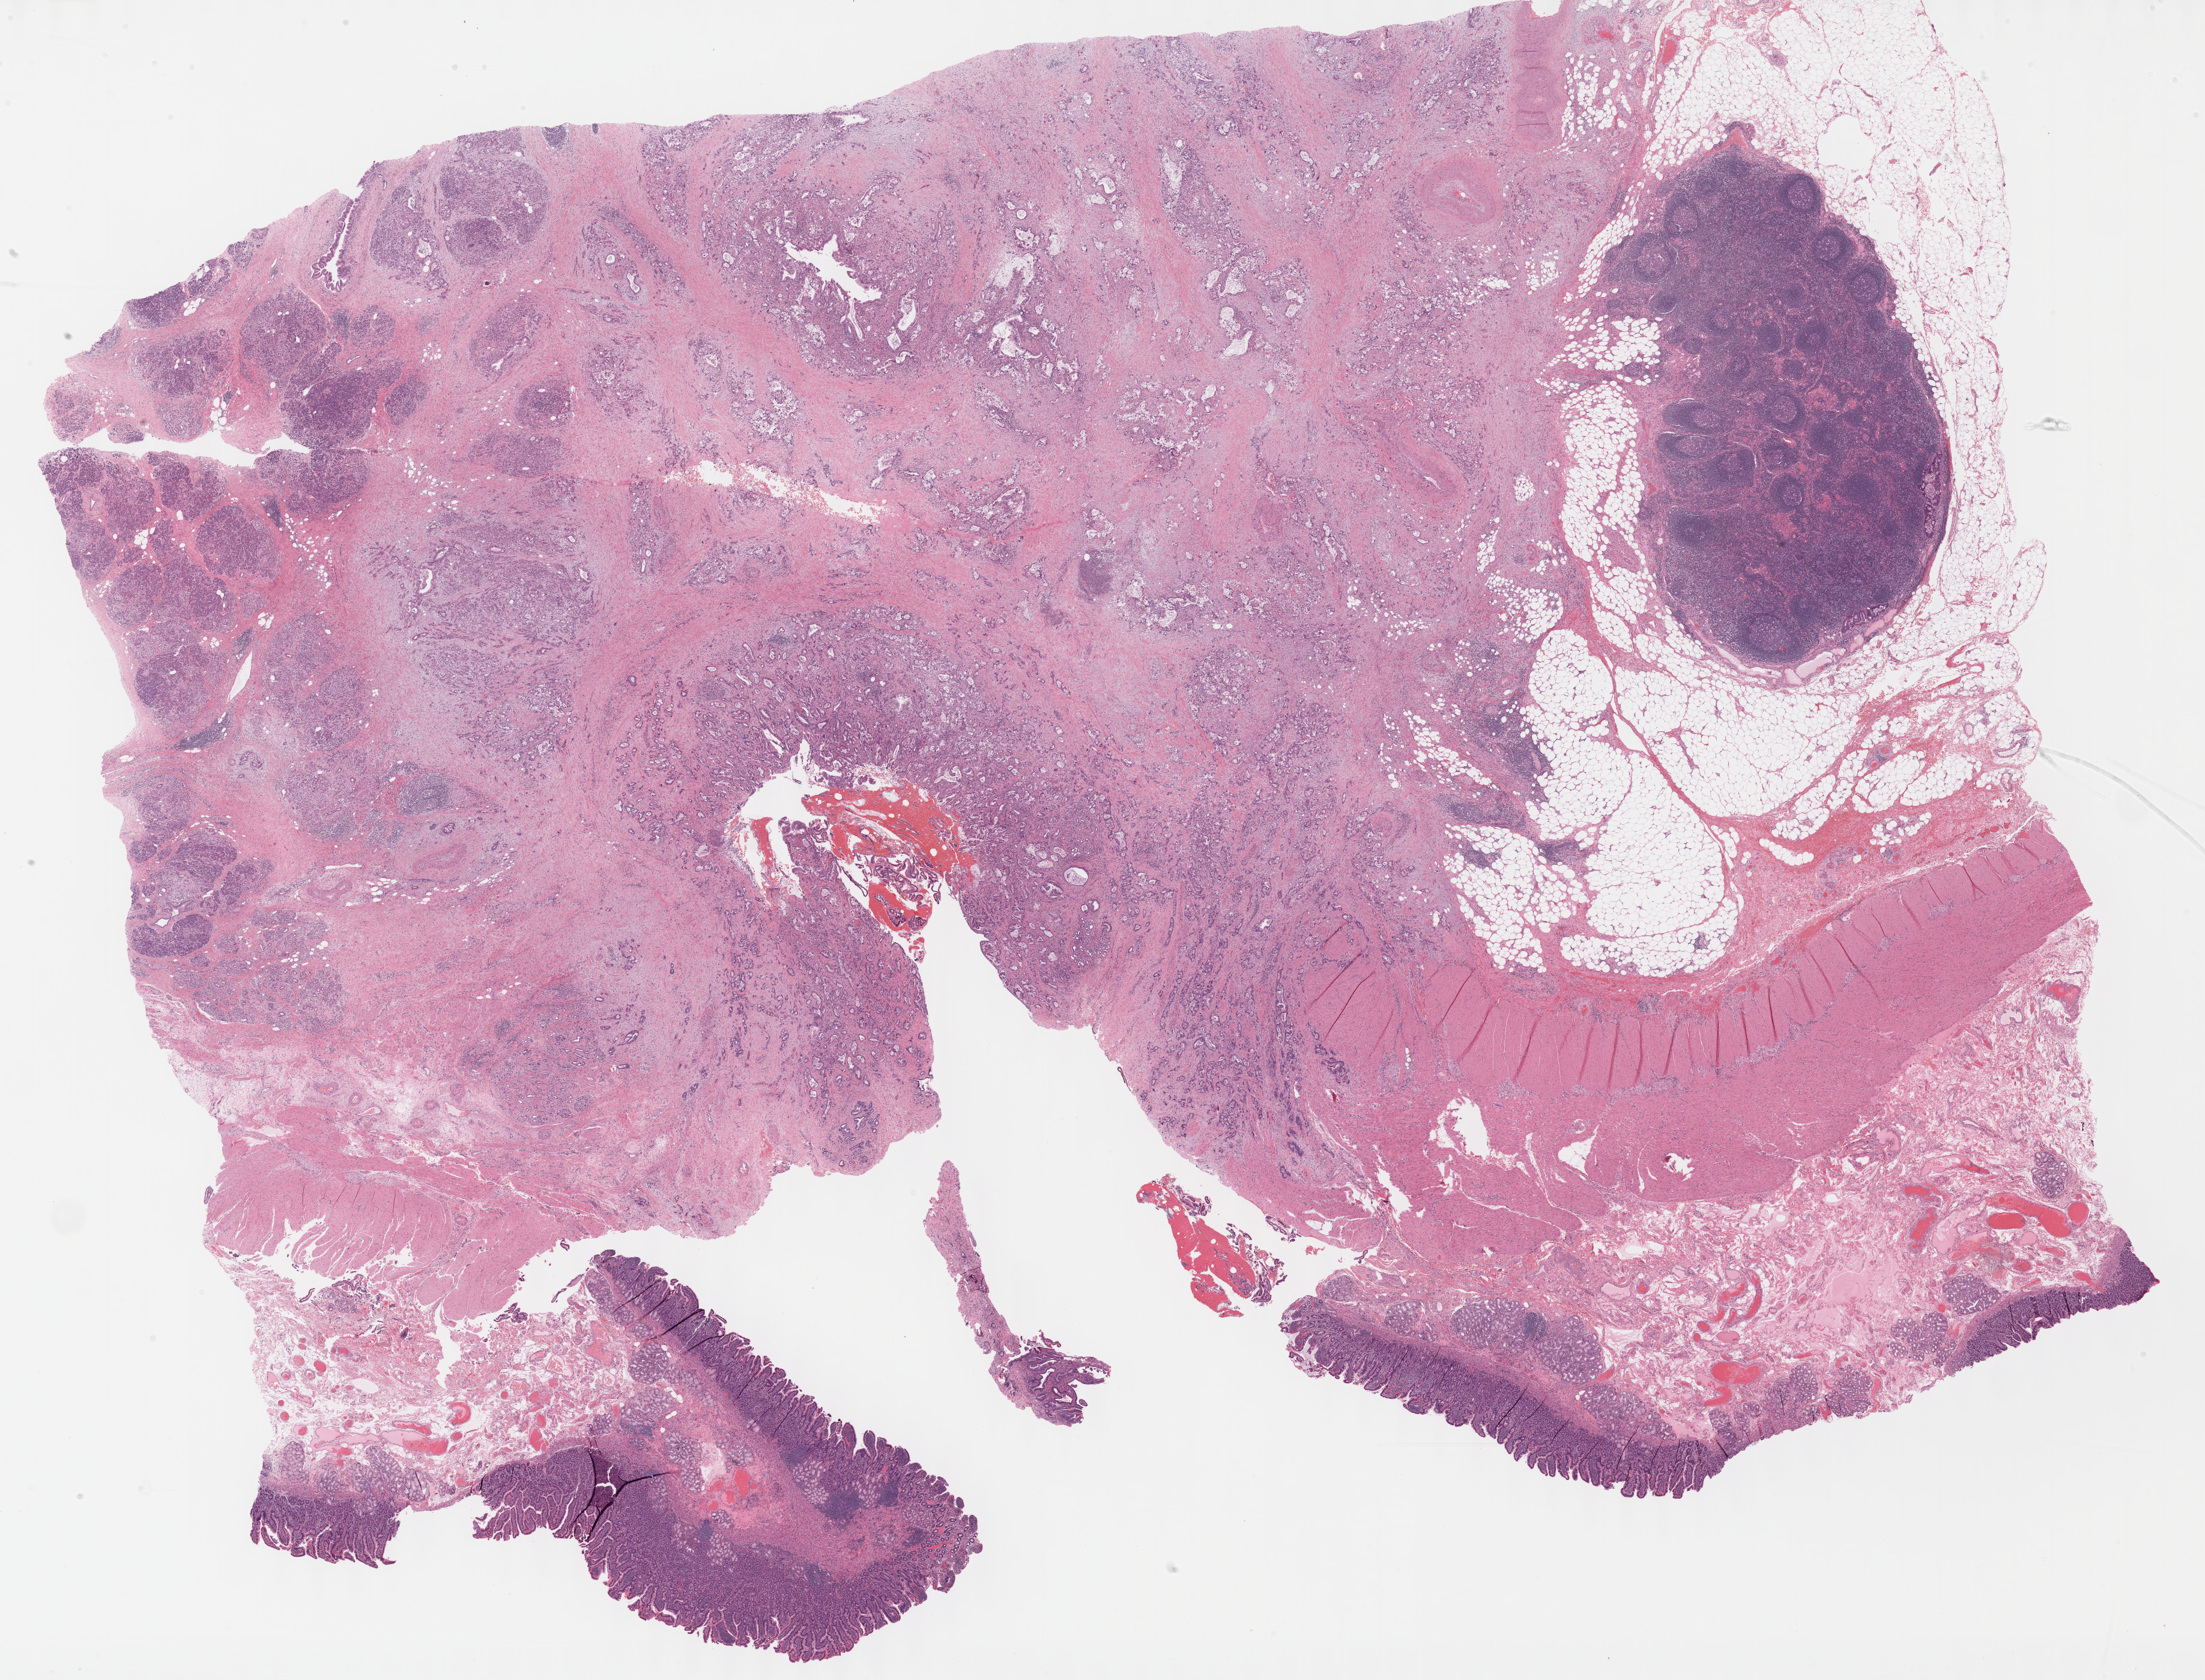
Whole-slide histology image, H&E-stained, low-resolution overview of the scanned area, about 29.7 x 22.6 mm. FFPE section. Sample: primary tumour, bile duct. Female, age 70 years at initial diagnosis.
Diagnosis: Cholangiocarcinoma (extrahepatic bile duct).